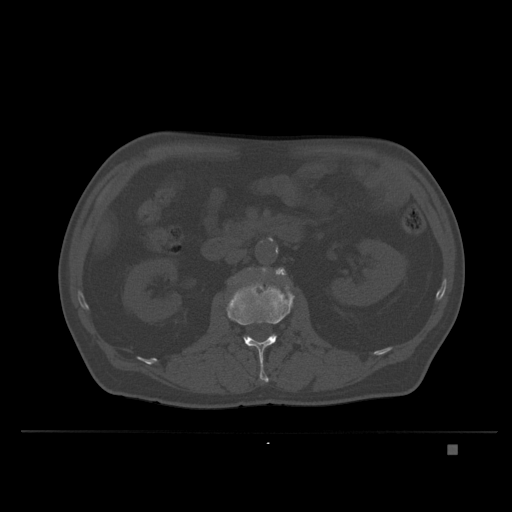
CT including the spine, one axial slice; bone window (W 1800 / L 400 HU); 1.5 mm slice thickness; 512 × 512 image matrix, field of view 434 × 434 mm. Patient: male, 73 years. Case-level facts recorded for this patient, not image findings: primary cancer: skin.
Annotated regions visible in this slice (semi-automatic segmentation, software-assisted and operator-edited):
- L2 vertebra: bounding box [x1, y1, x2, y2] px = [226, 274, 300, 384]
- L3 vertebra: [248, 267, 286, 276]